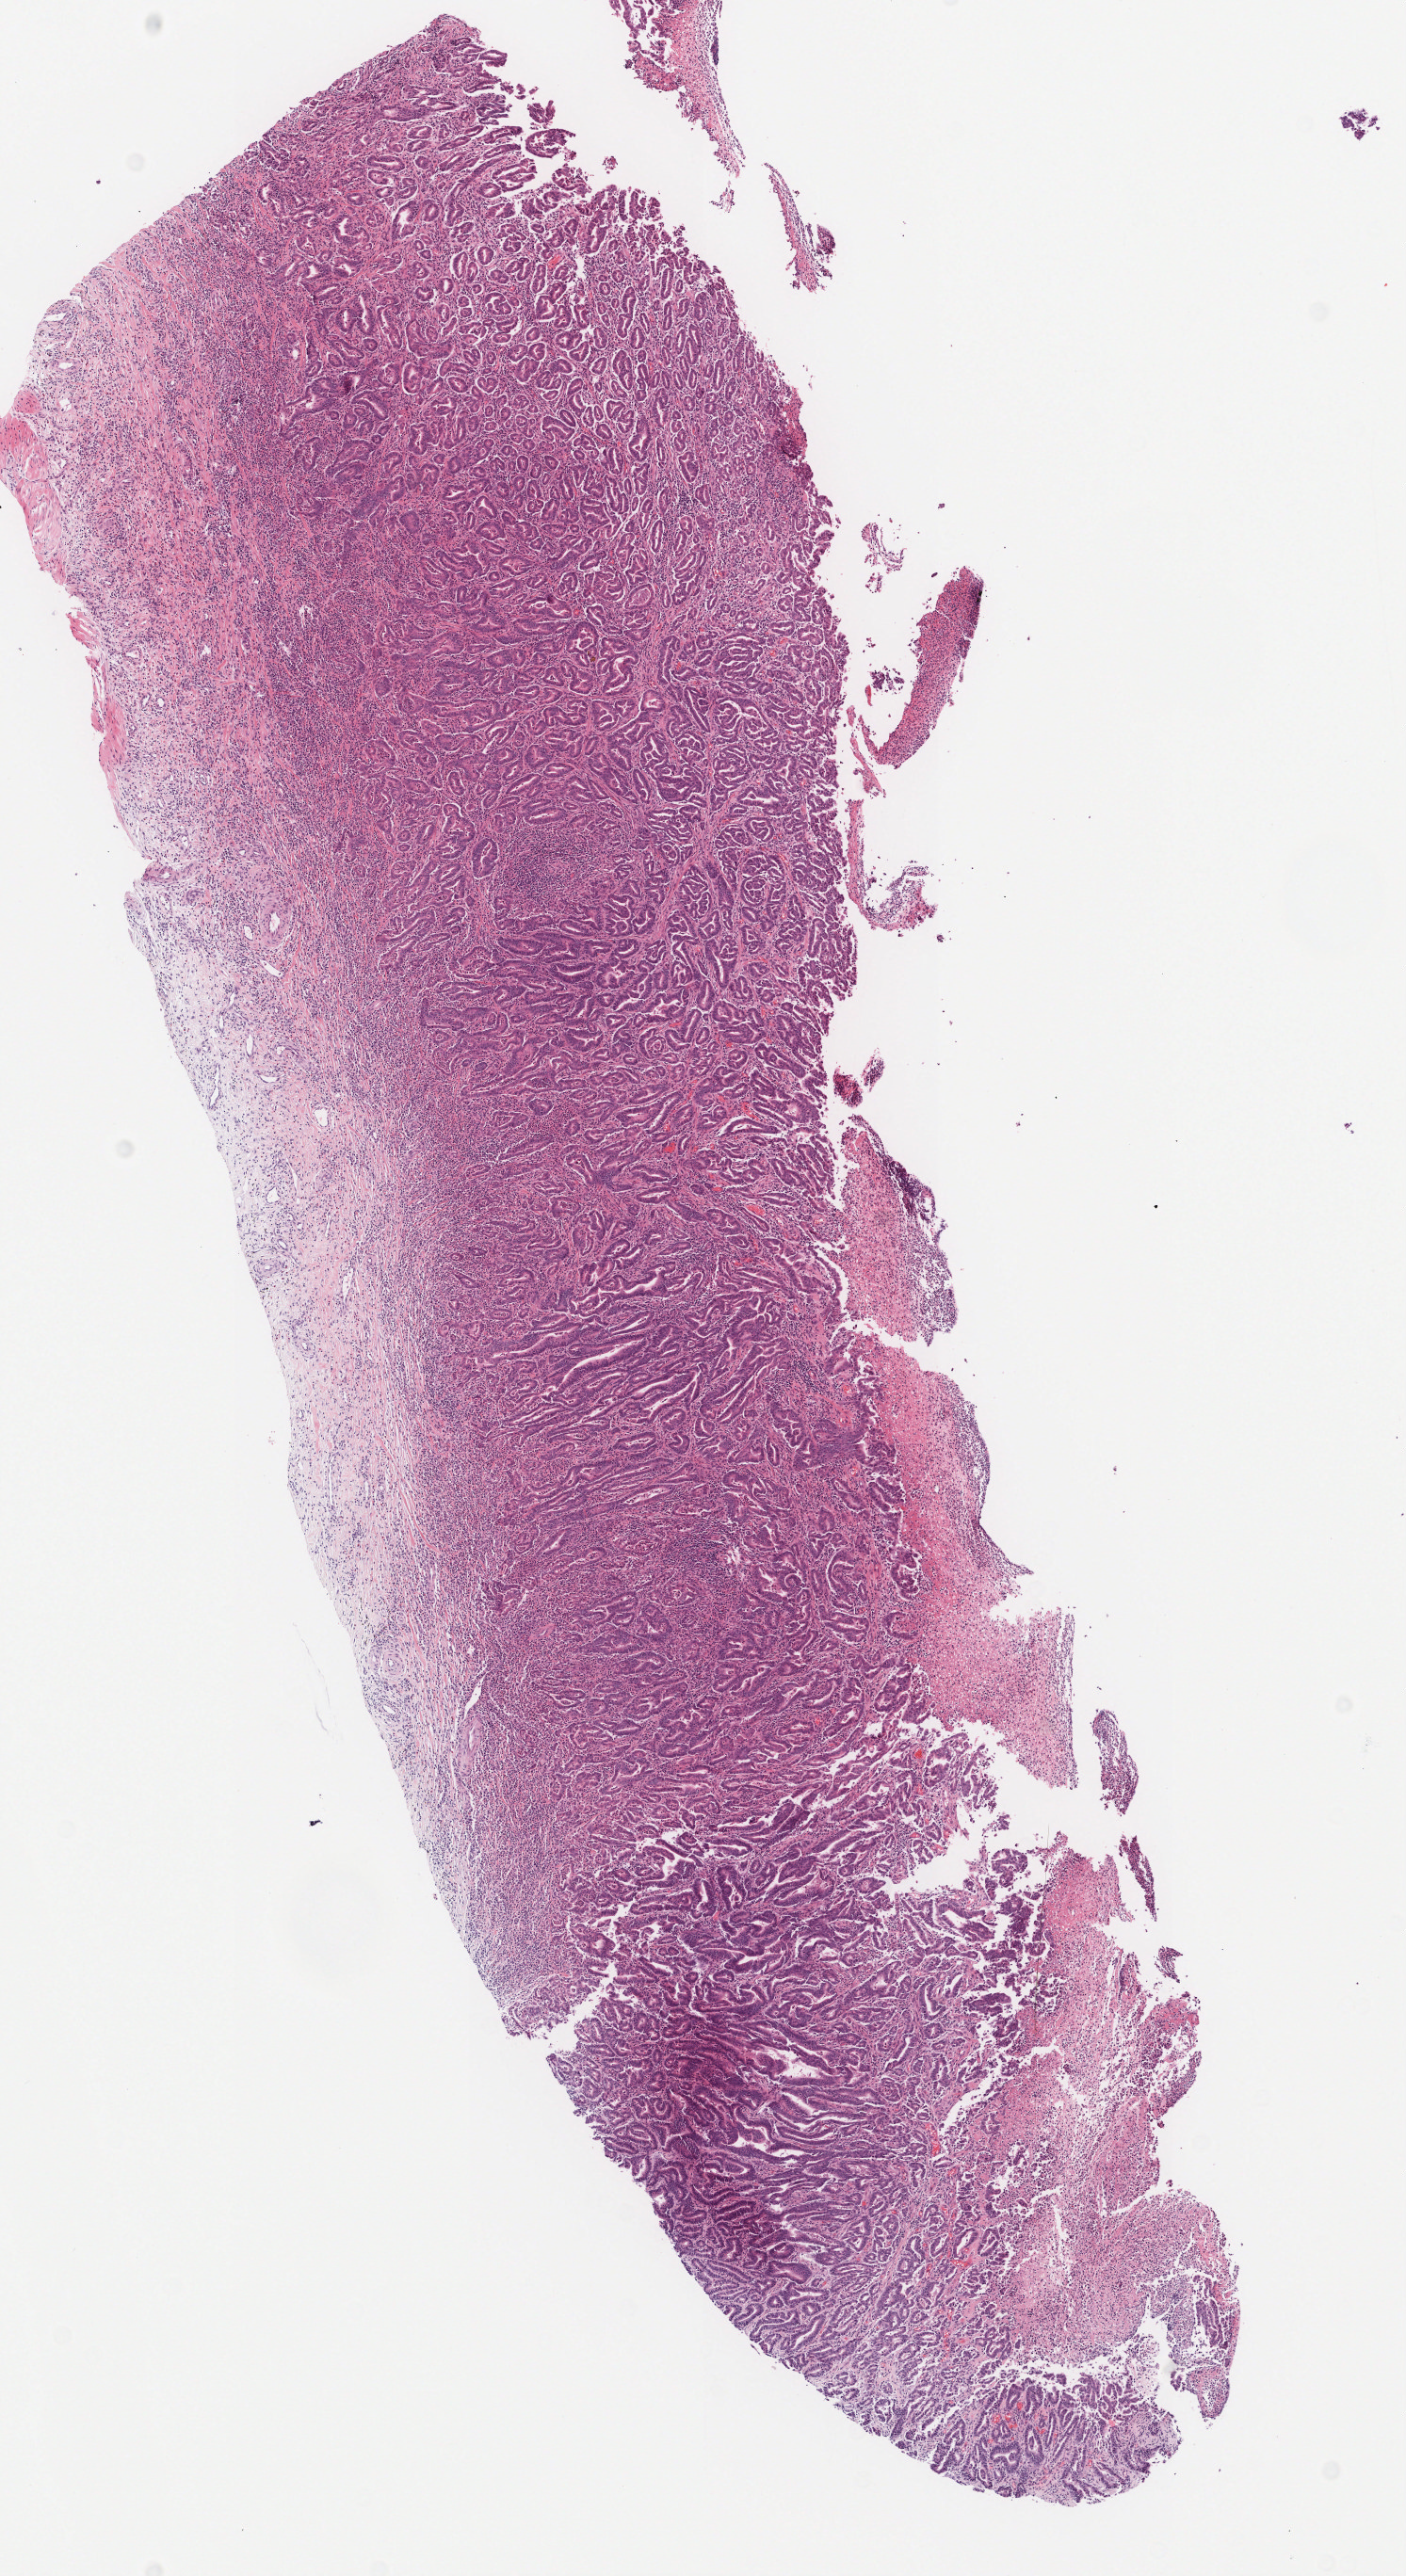
Whole-slide histology image, H&E-stained, low-resolution overview of the scanned area, about 5.9 x 10.8 mm. Formalin-fixed paraffin-embedded (FFPE) diagnostic section. Sample: primary tumour, stomach. Male, age 61 years at initial diagnosis. Histologic grade: G2 (moderately differentiated).
- TNM: T2 N1 M0
- AJCC pathologic stage: IIA (7th edition)
- lymph nodes positive (case pathology): 1 of 47 examined
- diagnosis: Tubular adenocarcinoma (gastric antrum)